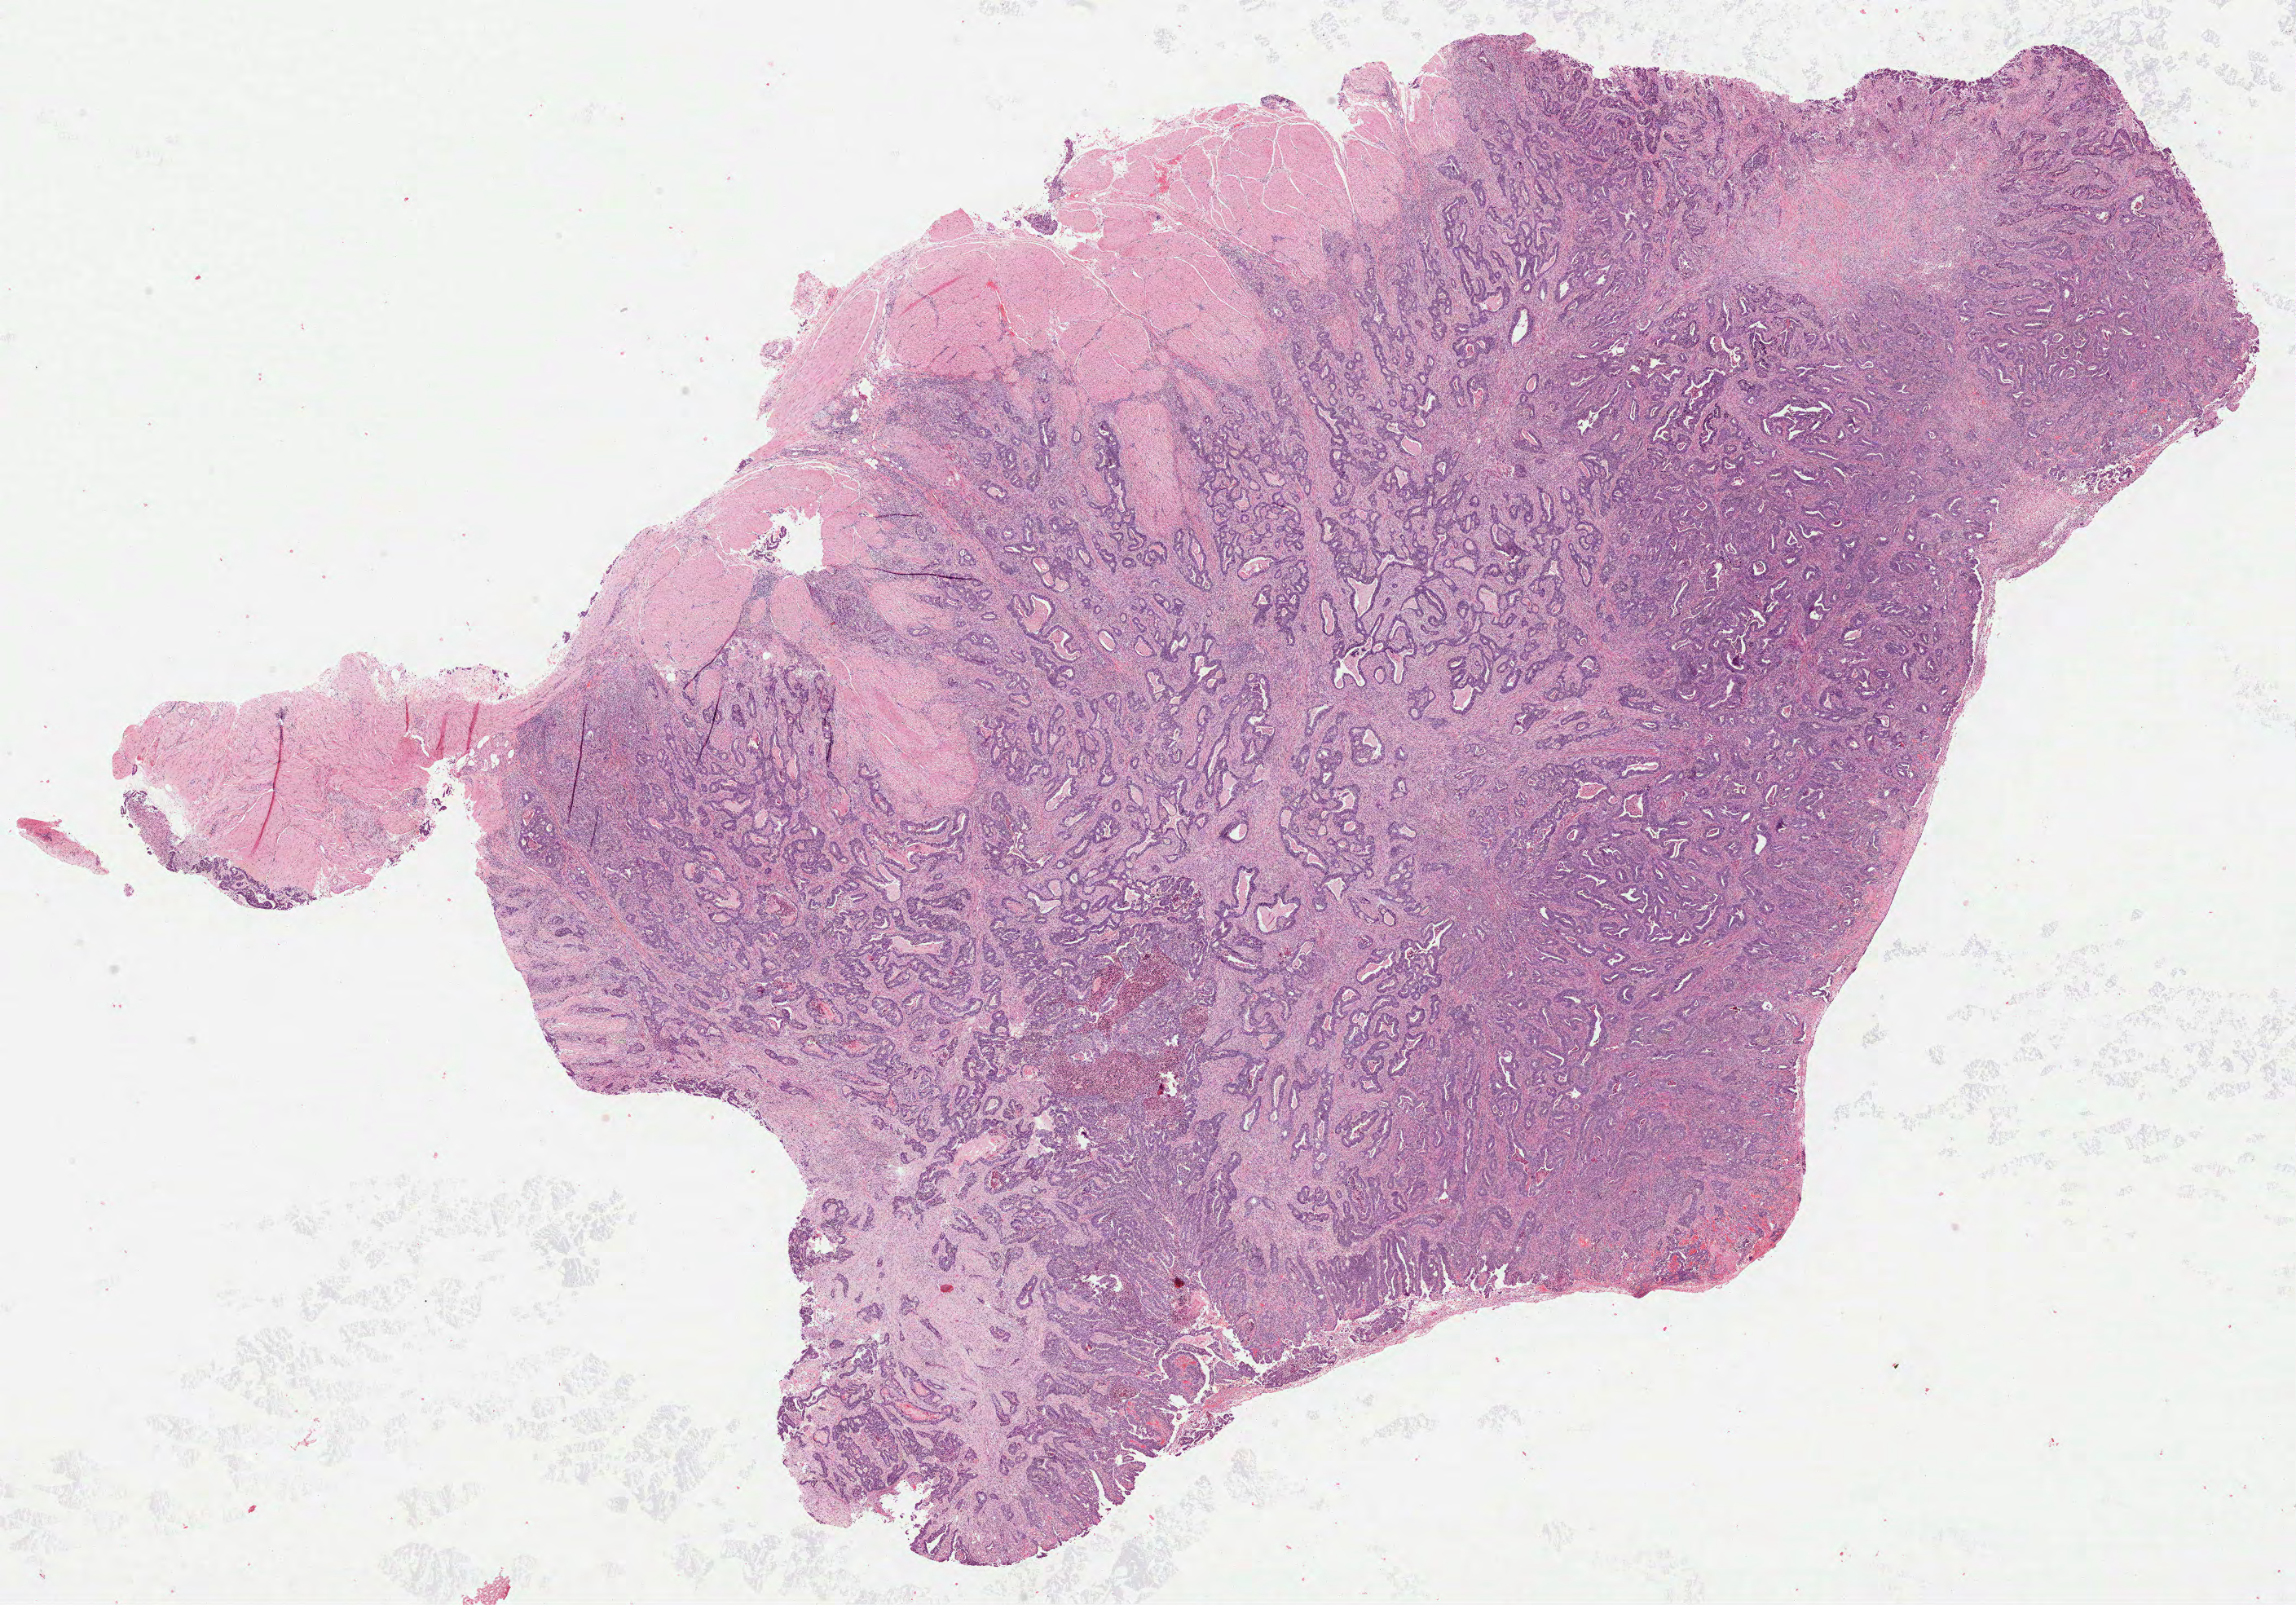
H&E whole-slide image — whole scanned area (about 22.7 x 15.9 mm, from a 40x scan) shown as a low-resolution overview; formalin-fixed paraffin-embedded (FFPE) diagnostic section; stomach, primary tumour sample. Male, age 67 years at initial diagnosis. Histologic grade: G2 (moderately differentiated).
TNM: T4a N0 M0. AJCC pathologic stage: IIB (7th edition). Pathologic diagnosis: Adenocarcinoma, NOS.